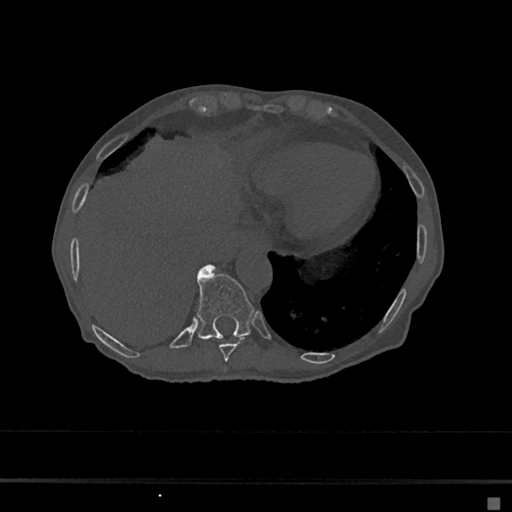
CT including the spine, one axial slice; slice 242 of 797 in the series (ordered by position); 120 kVp; bone window (W 1800 / L 400 HU); 512 × 512 image matrix. Patient: female, 68 years. Case-level facts recorded for this patient, not image findings: primary cancer: renal.
Structures marked on this image (semi-automatic segmentation, software-assisted and operator-edited):
- T10 vertebra: box from (x=197, y=265) to (x=254, y=339) px
- T9 vertebra: (x=219, y=337)–(x=245, y=362)